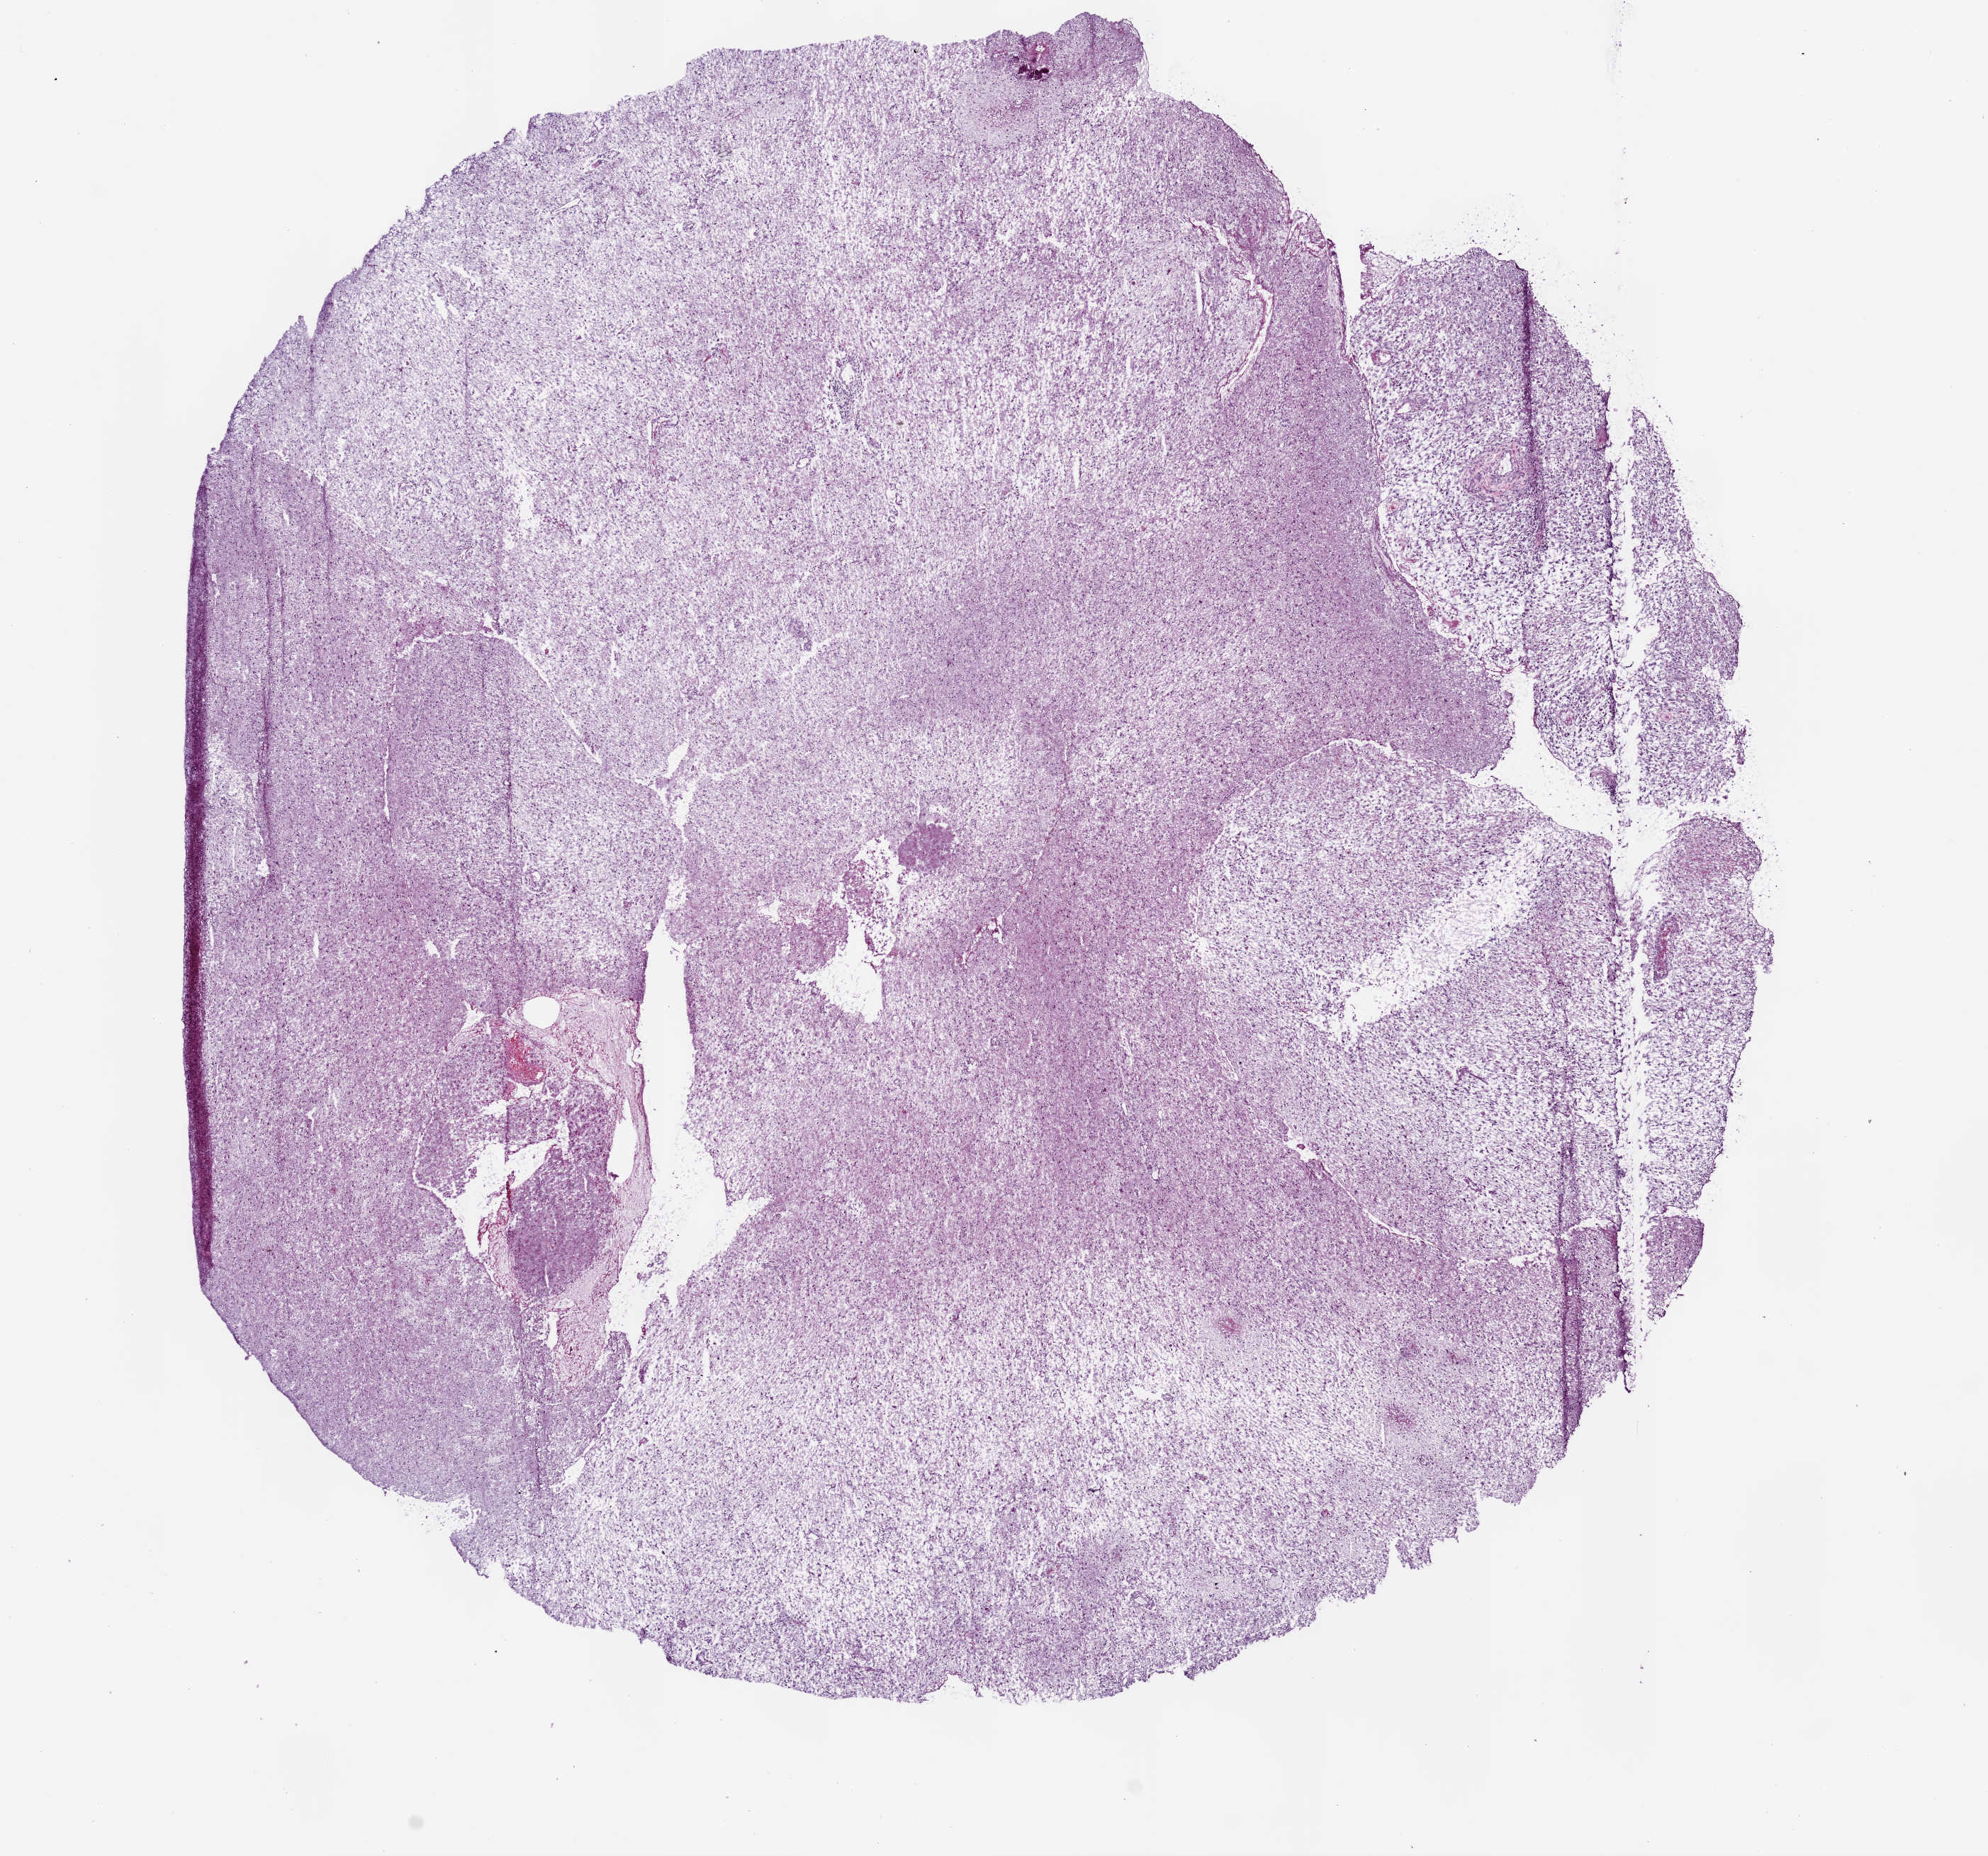
H&E whole-slide image — a low-resolution overview of the entire scanned area, about 11.2 x 10.5 mm (acquisition: 5x scan); frozen section from the bottom of the tissue portion; sample: primary tumour, brain. Female, age 72 years at initial diagnosis.
Pathologic diagnosis: Glioblastoma.